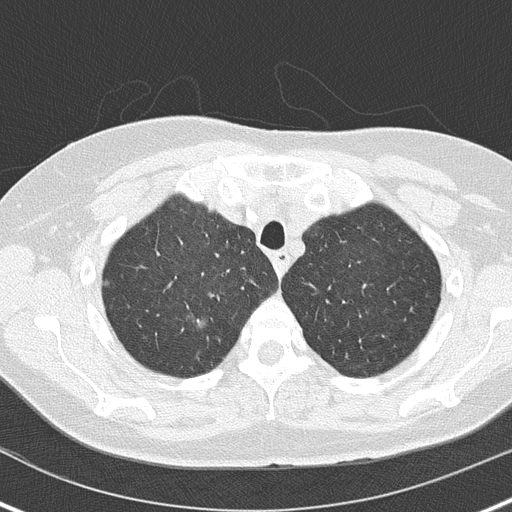
Axial slice from a low-dose chest CT screening exam, baseline annual screen, lung window (W 1500 / L -600 HU), 2 mm slice thickness, 512 × 512 image matrix, field of view 300 × 300 mm. Female participant, aged 61 years at enrolment.
Expert-annotated lung lesion, bounding box (x1, y1, x2, y2) in pixels: (183, 308, 217, 338). Reader record for this screening exam (exam-level; its link to the box is not recorded): non-calcified nodule or mass ≥4 mm, right upper lobe, 8 × 5 mm, smooth margins, soft tissue attenuation. Official screen result: positive, change unspecified: nodule(s) >= 4 mm or enlarging nodule(s), mass(es), or other non-specific abnormalities suspicious for lung cancer.